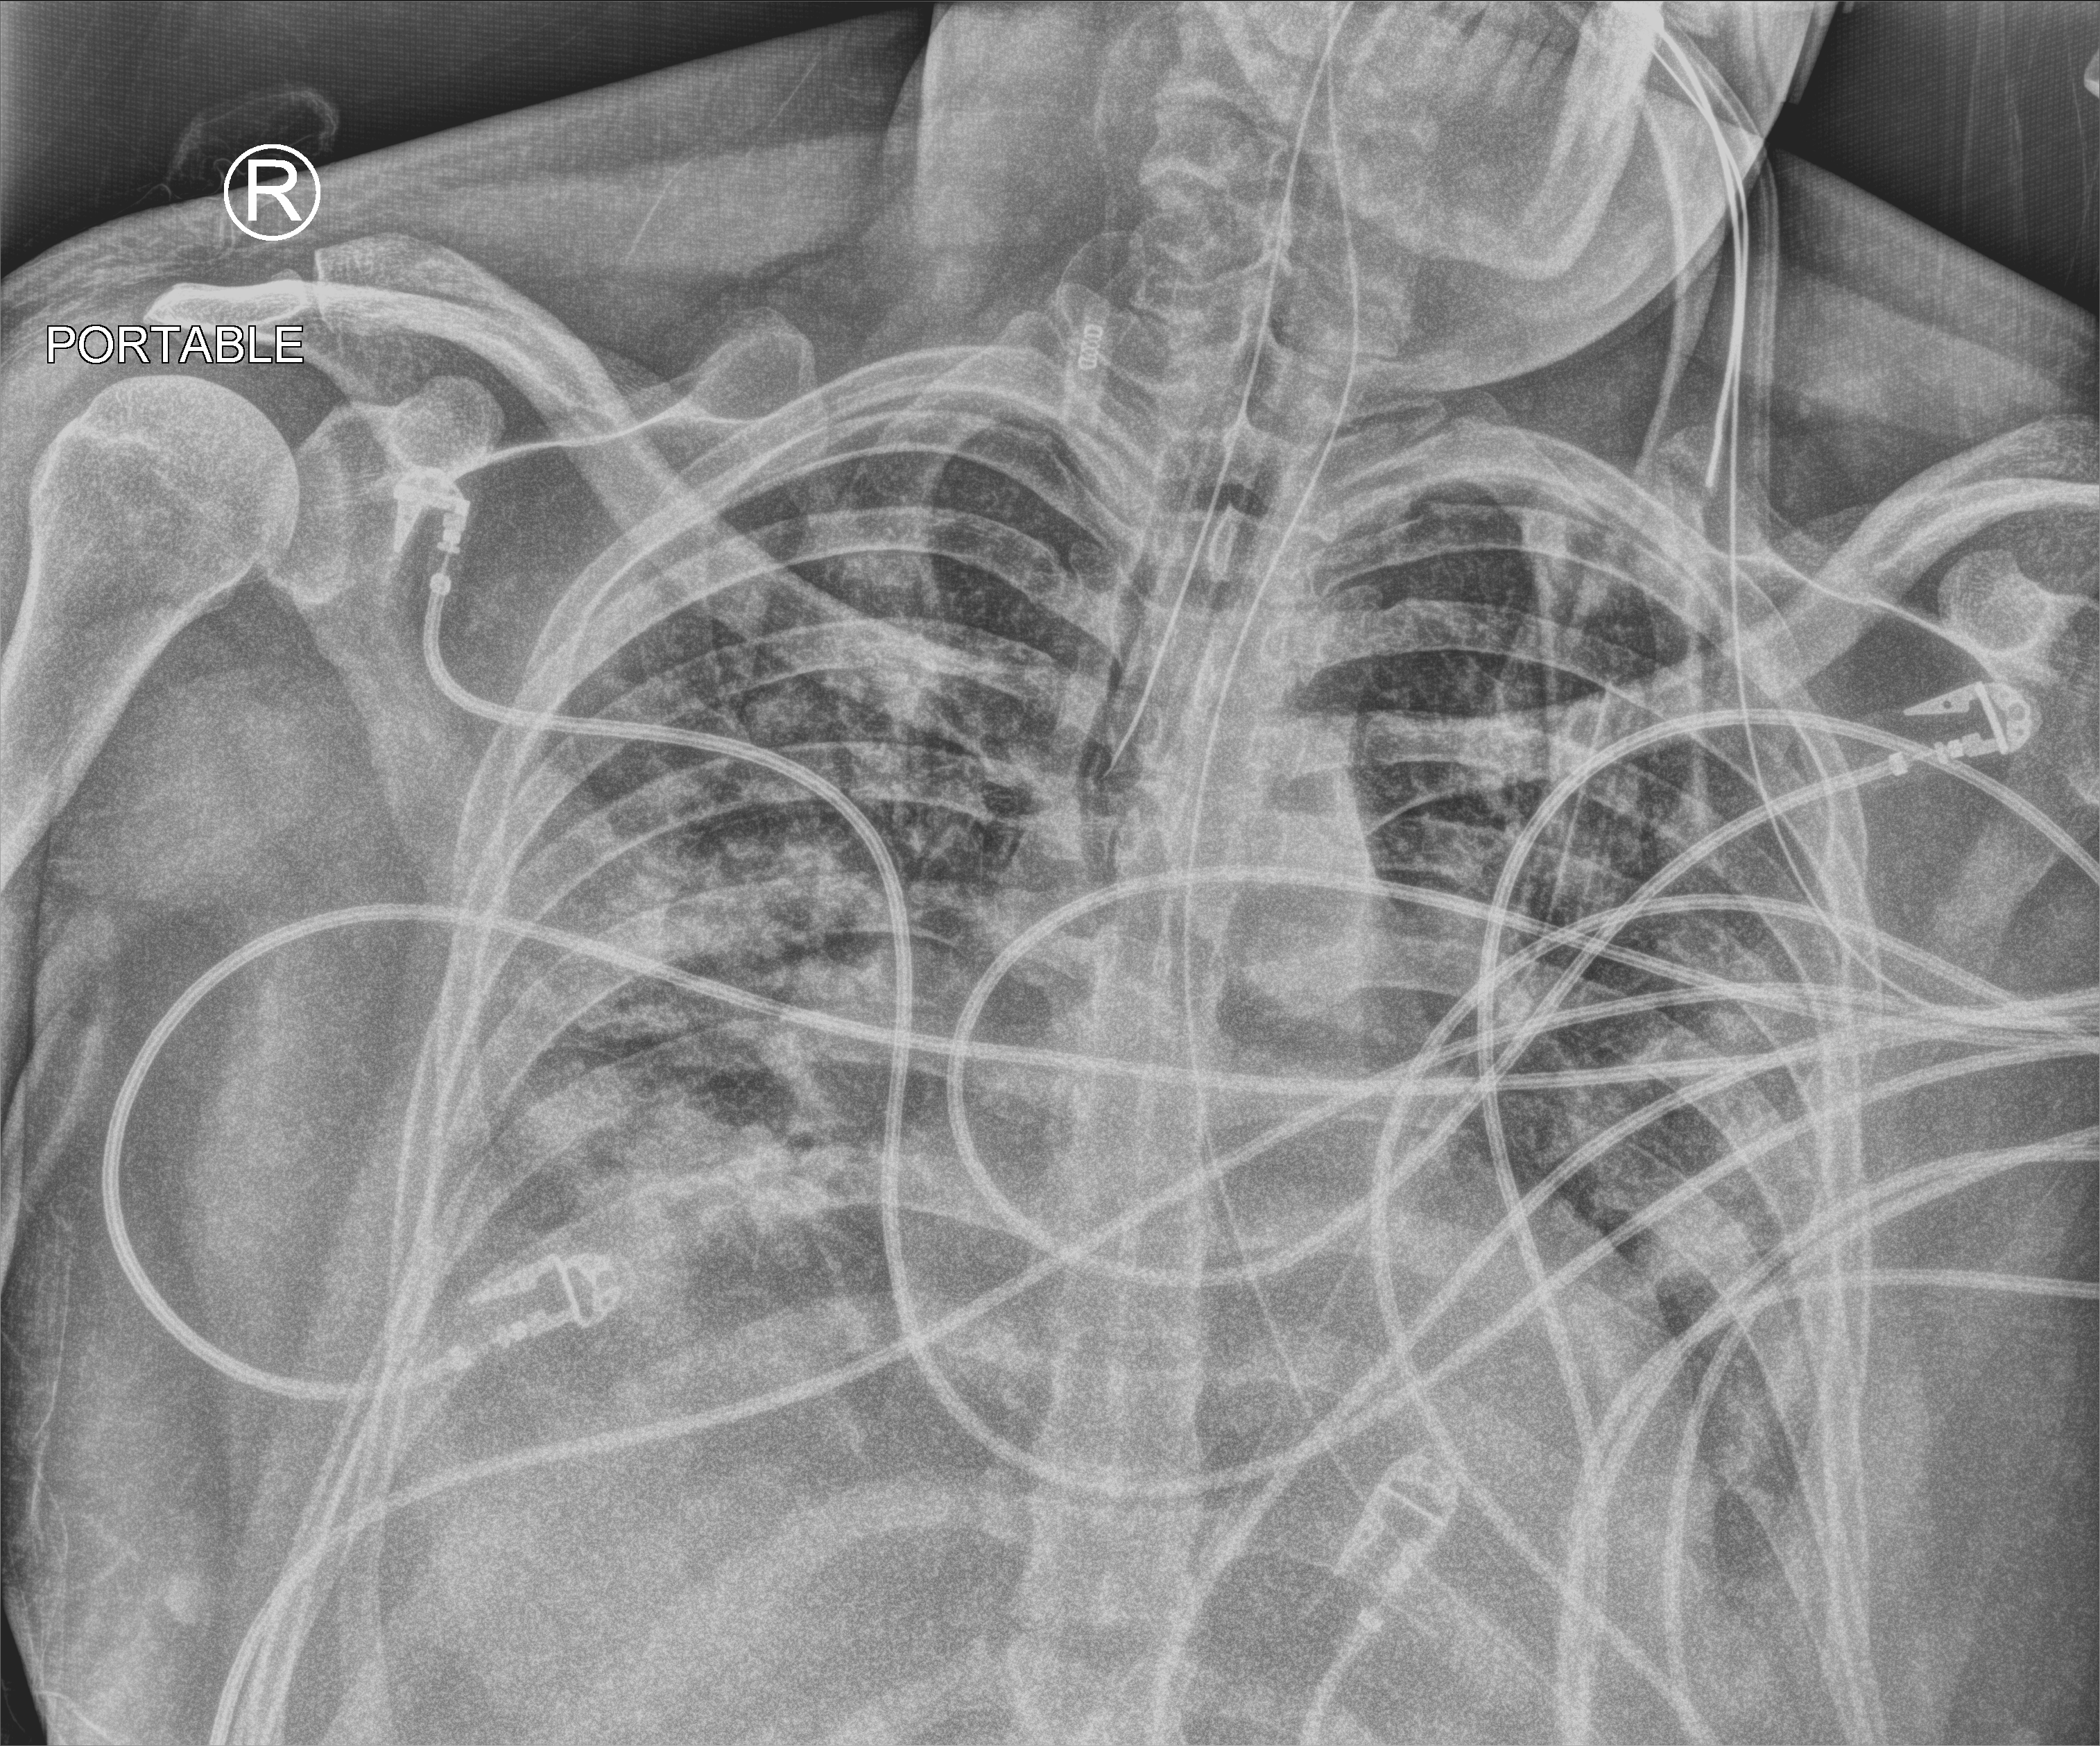
Bedside chest radiograph (computed radiography); anteroposterior (AP) projection. Male patient hospitalised with COVID-19, age 18–59 years.
From the hospital-stay record, not from the radiograph (when in the stay this image was taken is not recorded):
- admitted to intensive care during this hospital stay: yes
- mechanically ventilated during this hospital stay: yes